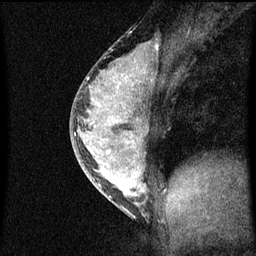
Breast MRI (dynamic contrast-enhanced), one sagittal slice; slice 32 of 60 in the series (ordered by position); dynamic contrast-enhanced series, image 2 of 3 at this slice position (ordered by acquisition); 1.5 T; TE 4.2 ms, TR 8 ms; 2 mm slice thickness; 256 × 256 image matrix, field of view 180 × 180 mm. Female patient, age 33 years.
Outlined on this slice (semi-automatically segmented with operator editing):
- analysis volume of interest (the breast-tissue region the enhancement analysis was run in; not a lesion): bounding box [x1, y1, x2, y2] px = [70, 56, 160, 215]
- tumour enhancement mask (voxels above the 70 % enhancement threshold inside the analysis volume of interest): [88, 60, 147, 205]